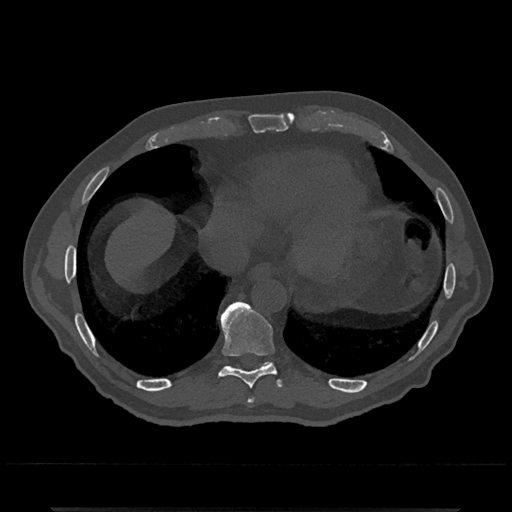
CT including the spine, one axial slice. Position 605 of 797 along the scan axis. 120 kVp. Bone window (W 1800 / L 400 HU). 0.5 mm slice thickness. 512 × 512 image matrix. Patient: male, 67 years. From the clinical record (not read from this slice): primary cancer: prostate.
Outlined on this slice (semi-automatically segmented with operator editing):
- T10 vertebra: bounding box [x1, y1, x2, y2] px = [264, 362, 269, 365]
- T8 vertebra: [248, 397, 254, 403]
- T9 vertebra: [219, 301, 282, 389]